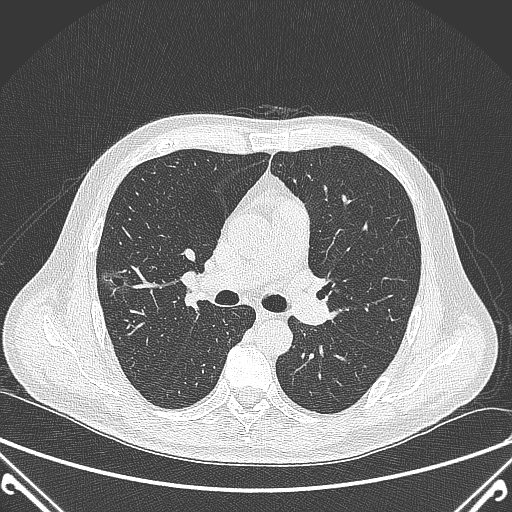
Chest CT, one axial slice. 120 kVp. Lung window (W 1500 / L -600 HU). 1 mm slice thickness. 512 × 512 image matrix, field of view 380 × 380 mm. Patient: male, 64 years. From the clinical record (not read from this slice): clinical TNM (as recorded): T1c N0 M0; histopathological grade: G2.
Annotated regions visible in this slice (bounding box drawn by a radiologist):
- lung tumour (recorded histology: adenocarcinoma): bounding box [x1, y1, x2, y2] px = [93, 260, 142, 298]